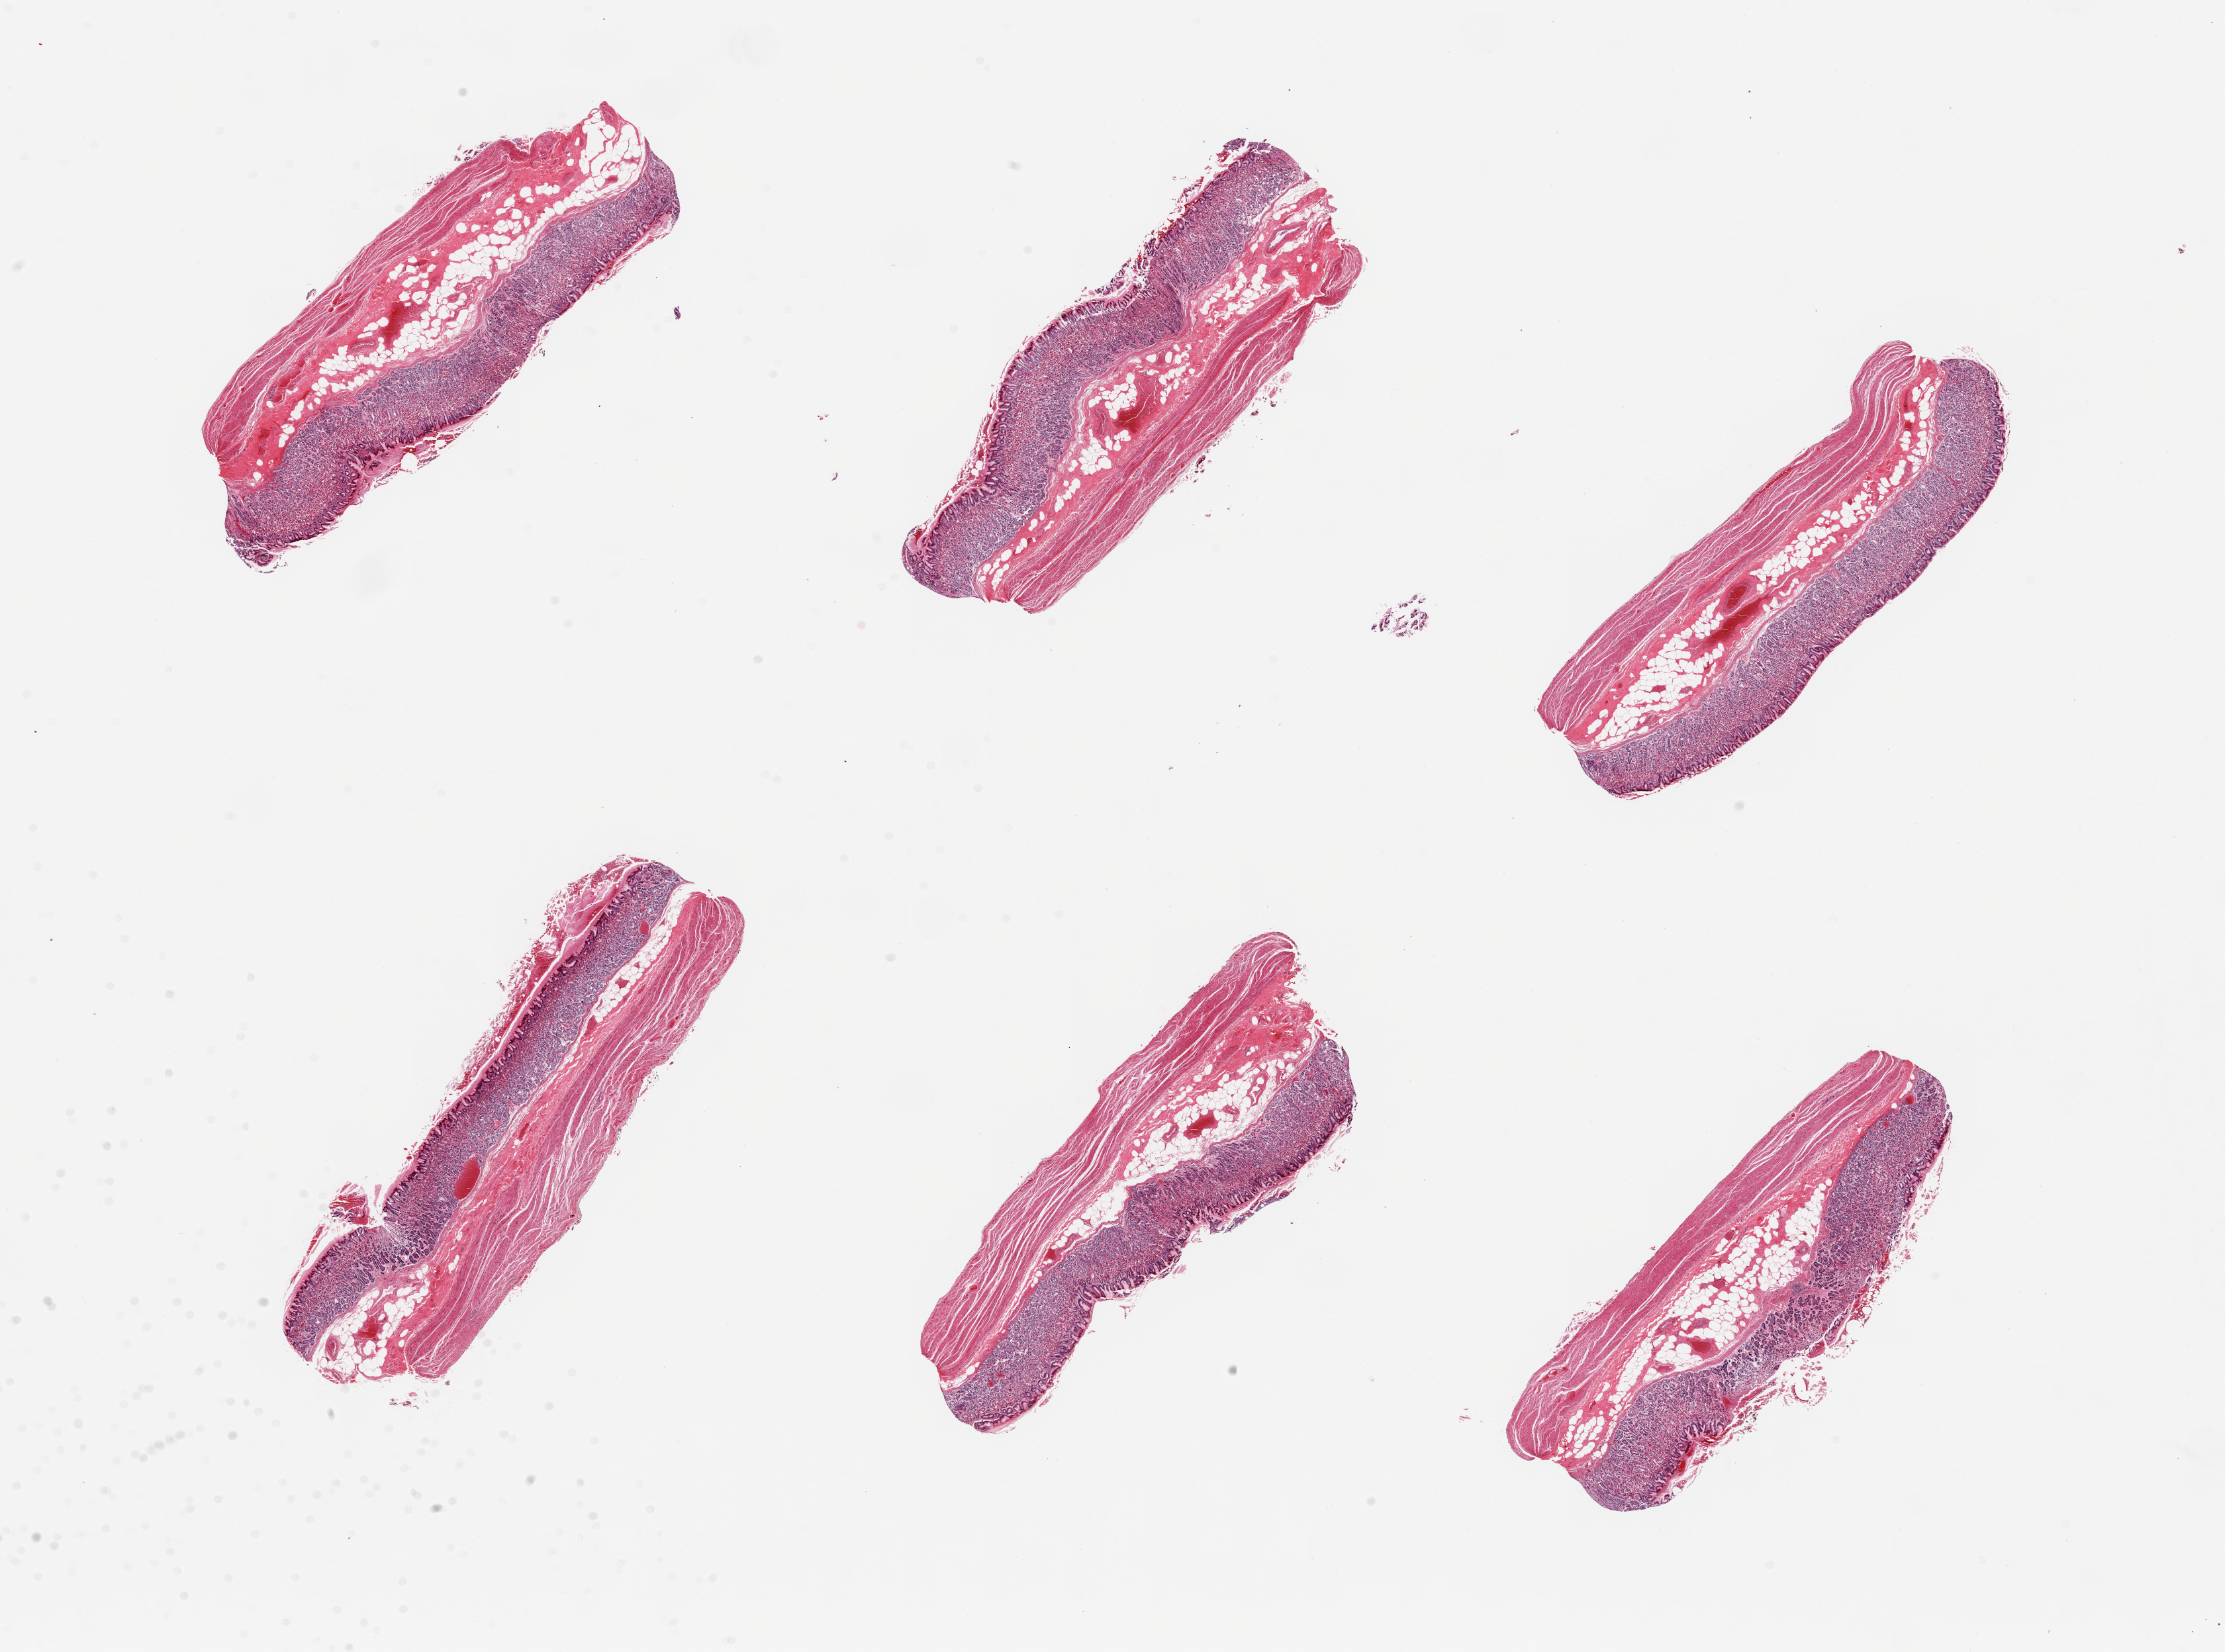
Haematoxylin and eosin whole-slide image — low-resolution overview of the scanned area, about 26.6 x 19.7 mm (from a 20x scan); PAXgene-fixed paraffin-embedded (PFPE) section; target tissue: stomach; donor tissue sample. Donor sex: male.
* reviewer comment on this tissue sample: 6 pieces, mucosa is ~0.7mm, ~30-40% thickness, mild-moderate autolysis, areas approach score '2'